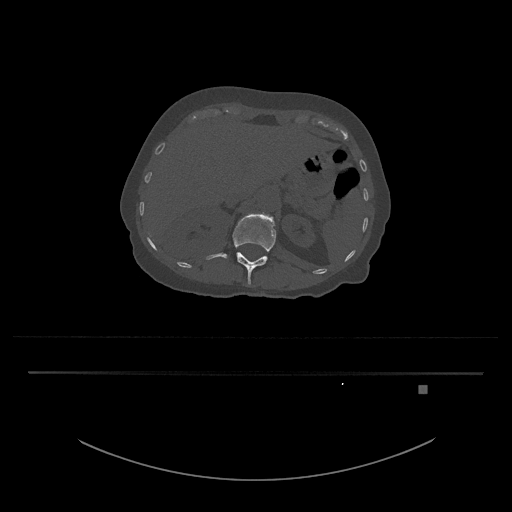
CT including the spine, one axial slice; slice 549 of 797 in the series (ordered by position); reconstruction kernel Br40s/3; 120 kVp; bone window (W 1800 / L 400 HU); 0.5 mm slice thickness; 512 × 512 image matrix. Patient: female, 57 years. From the clinical record (not read from this slice): primary cancer: cervical.
Annotated regions visible in this slice (semi-automatic segmentation, software-assisted and operator-edited):
- L1 vertebra: bounding box [x1, y1, x2, y2] px = [206, 213, 277, 285]